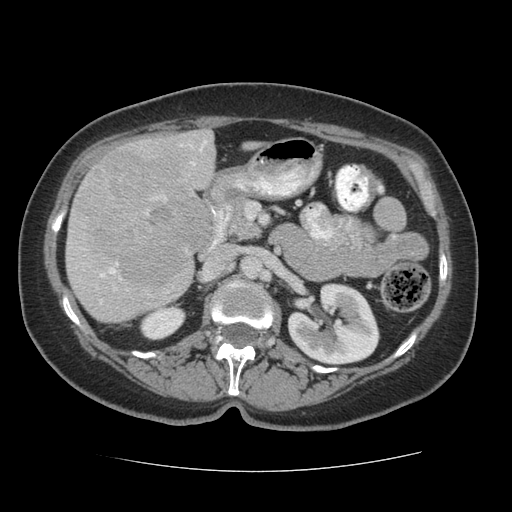
Contrast-enhanced abdominal CT (liver protocol), one axial slice; position 25 of 75 along the scan axis; reconstruction kernel STANDARD; soft-tissue window (W 400 / L 40 HU); 2.5 mm slice thickness; 512 × 512 image matrix. From the clinical record (not read from this slice): diagnosis: hepatocellular carcinoma (patient treated with transarterial chemoembolisation; whether this scan precedes or follows treatment is not stated here); TNM stage (as recorded): Stage-I; Child-Pugh class: A; tumour nodularity: uninodular.
Annotated regions visible in this slice (semi-automatic segmentation, software-assisted and operator-edited):
- liver parenchyma outside the tumour (the mass and vessels are separate outlines, so this box may not span the whole liver): box from (x=66, y=129) to (x=258, y=322) px
- mass: (x=70, y=147)–(x=212, y=297)
- liver vessels: (x=100, y=140)–(x=207, y=304)